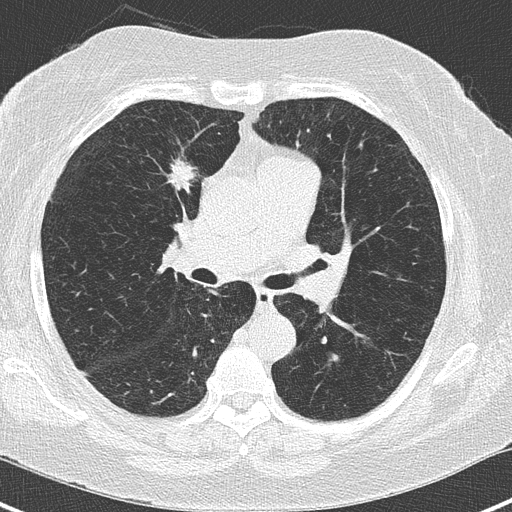
Chest CT (low-dose screening protocol), one axial image, third annual screen, lung window (W 1500 / L -600 HU), 2 mm slice thickness, slice 81 of 168 in the series. Female, age 62 years at enrolment. Current smoker at enrolment.
Expert reader's lesion annotation, bounding box <146,147,213,208> (left, top, right, bottom; pixels). The screening reader recorded 4 non-calcified nodules or masses ≥4 mm on this exam (right upper lobe, left lower lobe, left lower lobe); which of them this box marks is not recorded. Official screen result: positive, other. Later outcome: lung cancer diagnosed 41 days after this screen — adenocarcinoma, NOS, right upper lobe, moderately differentiated (G2), stage IA (AJCC 6th edition), 15 mm at pathology.